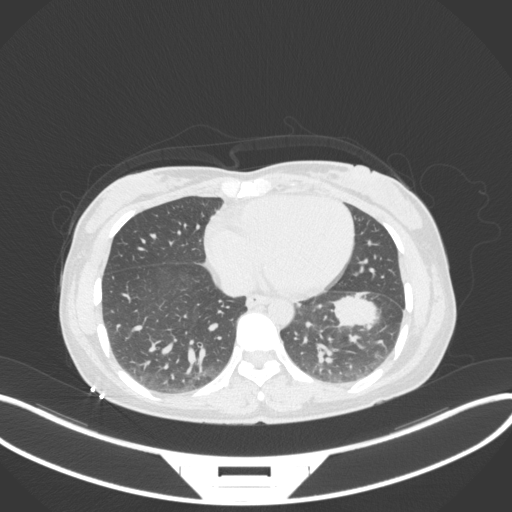
Chest CT, one axial slice; position 126 of 361 along the scan axis; reconstruction kernel B31f; 120 kVp; lung window (W 1500 / L -600 HU); 1 mm slice thickness; 512 × 512 image matrix, field of view 400 × 400 mm. Female patient, age 41 years. Case-level facts recorded for this patient, not image findings: clinical TNM (as recorded): T2a N3 M1b.
Outlined on this slice (bounding box drawn by a radiologist):
- lung tumour (recorded histology: adenocarcinoma): box from (x=332, y=291) to (x=379, y=336) px